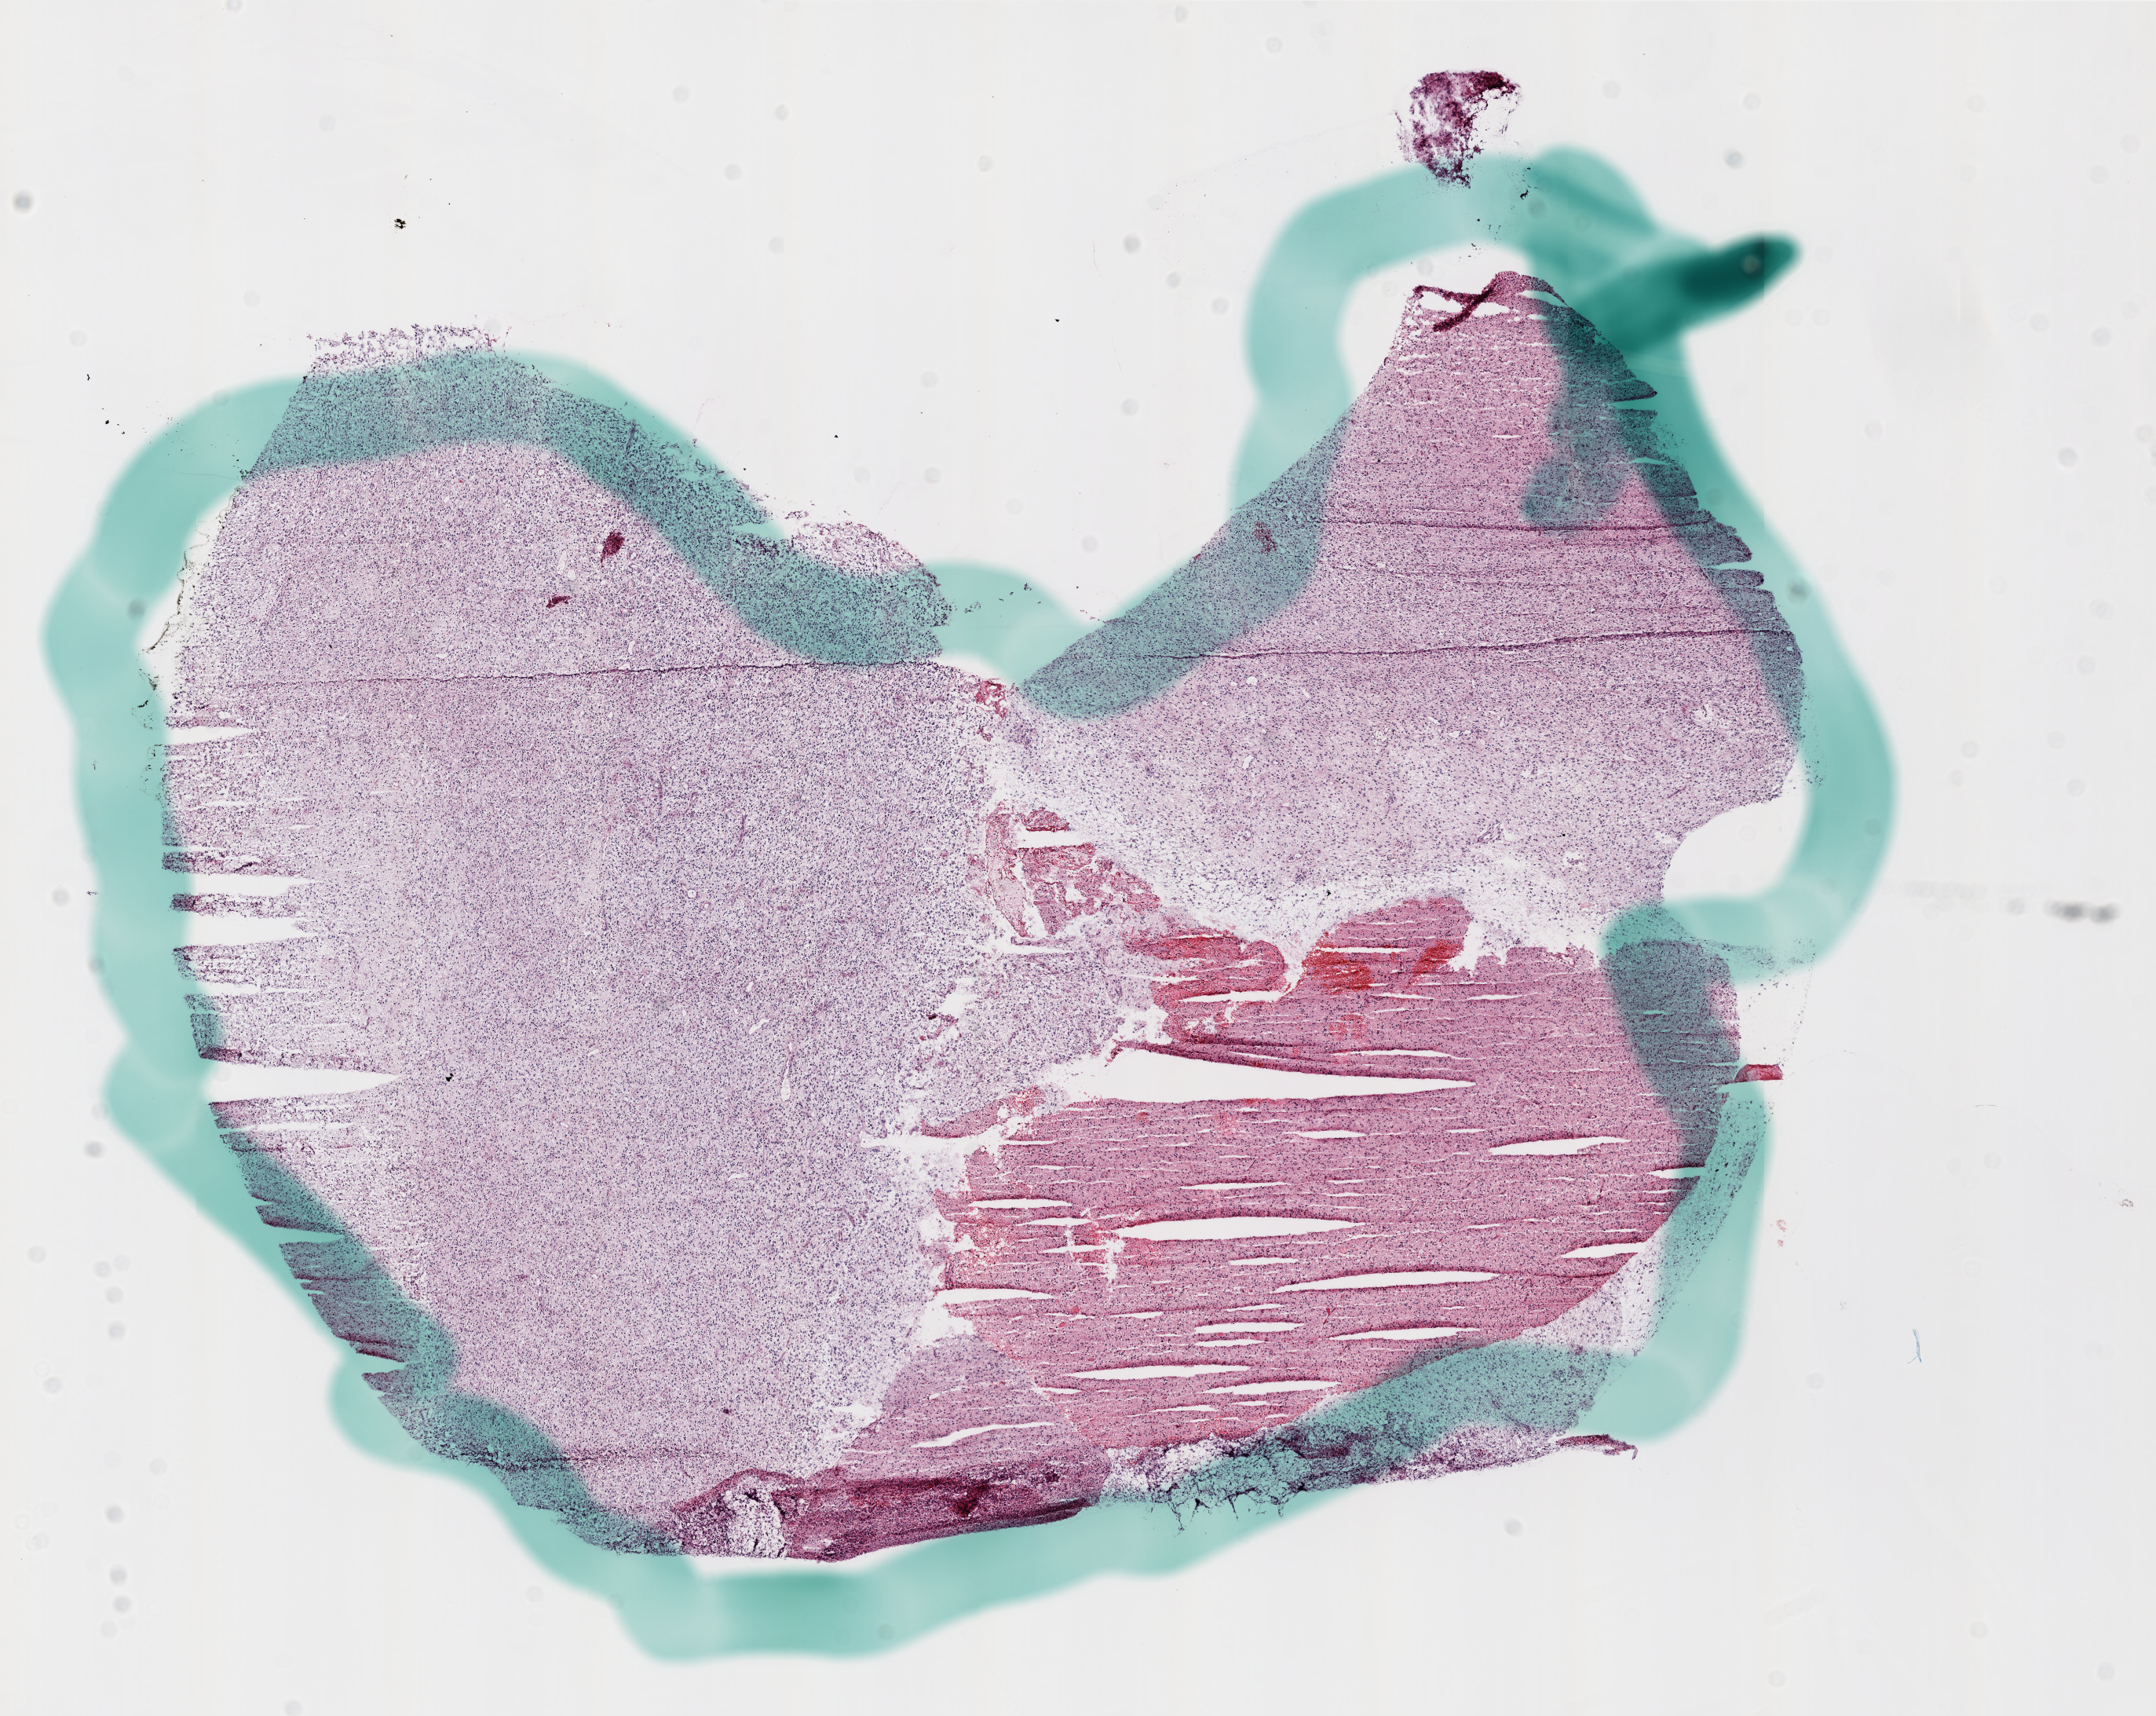
Hematoxylin and eosin (H&E) stained whole-slide image, a low-resolution overview of the entire scanned area, about 11.0 x 8.7 mm; frozen section; primary tumour sample from the brain. Patient: male, age at initial diagnosis 86 years. Pathologist review of this section (percent, as recorded): tumour cells 95%, tumour nuclei 100%, normal cells 5%, stromal cells 0%, necrosis 0%.
Histologic diagnosis: Glioblastoma.